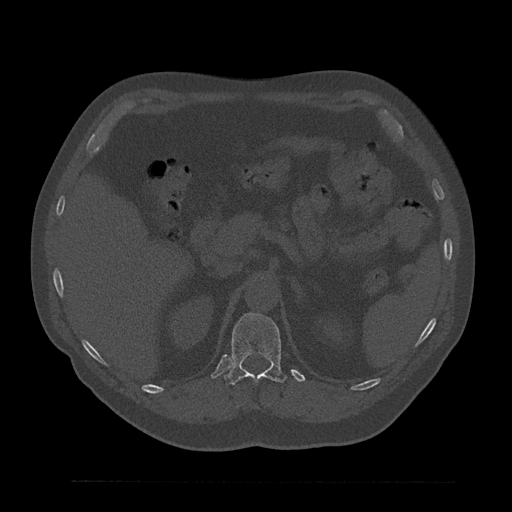
CT including the spine, one axial slice; slice 233 of 797 in the series (ordered by position); reconstruction kernel Br40s/3; bone window (W 1800 / L 400 HU); 0.5 mm slice thickness; 512 × 512 image matrix. Male patient, age 61 years. Case-level facts recorded for this patient, not image findings: primary cancer: prostate.
Outlined on this slice (semi-automatic segmentation, software-assisted and operator-edited):
- T12 vertebra: bounding box (x1, y1, x2, y2) in pixels: (224, 313, 287, 385)